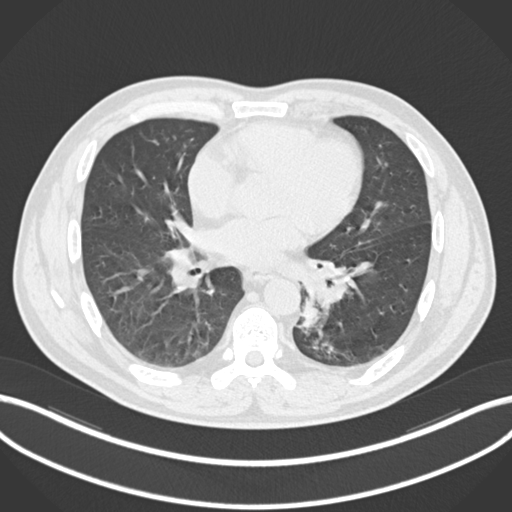
Chest CT, one axial slice. Slice 101 of 223 in the series (ordered by position). Reconstruction kernel B30f. 120 kVp. Lung window (W 1500 / L -600 HU). 512 × 512 image matrix, field of view 400 × 400 mm. Male patient, age 50 years. From the clinical record (not read from this slice): clinical TNM (as recorded): T2a N3 M0.
Outlined on this slice (rectangle marked by the reading radiologist):
- lung tumour (recorded histology: squamous cell carcinoma): box from (x=297, y=294) to (x=324, y=331) px